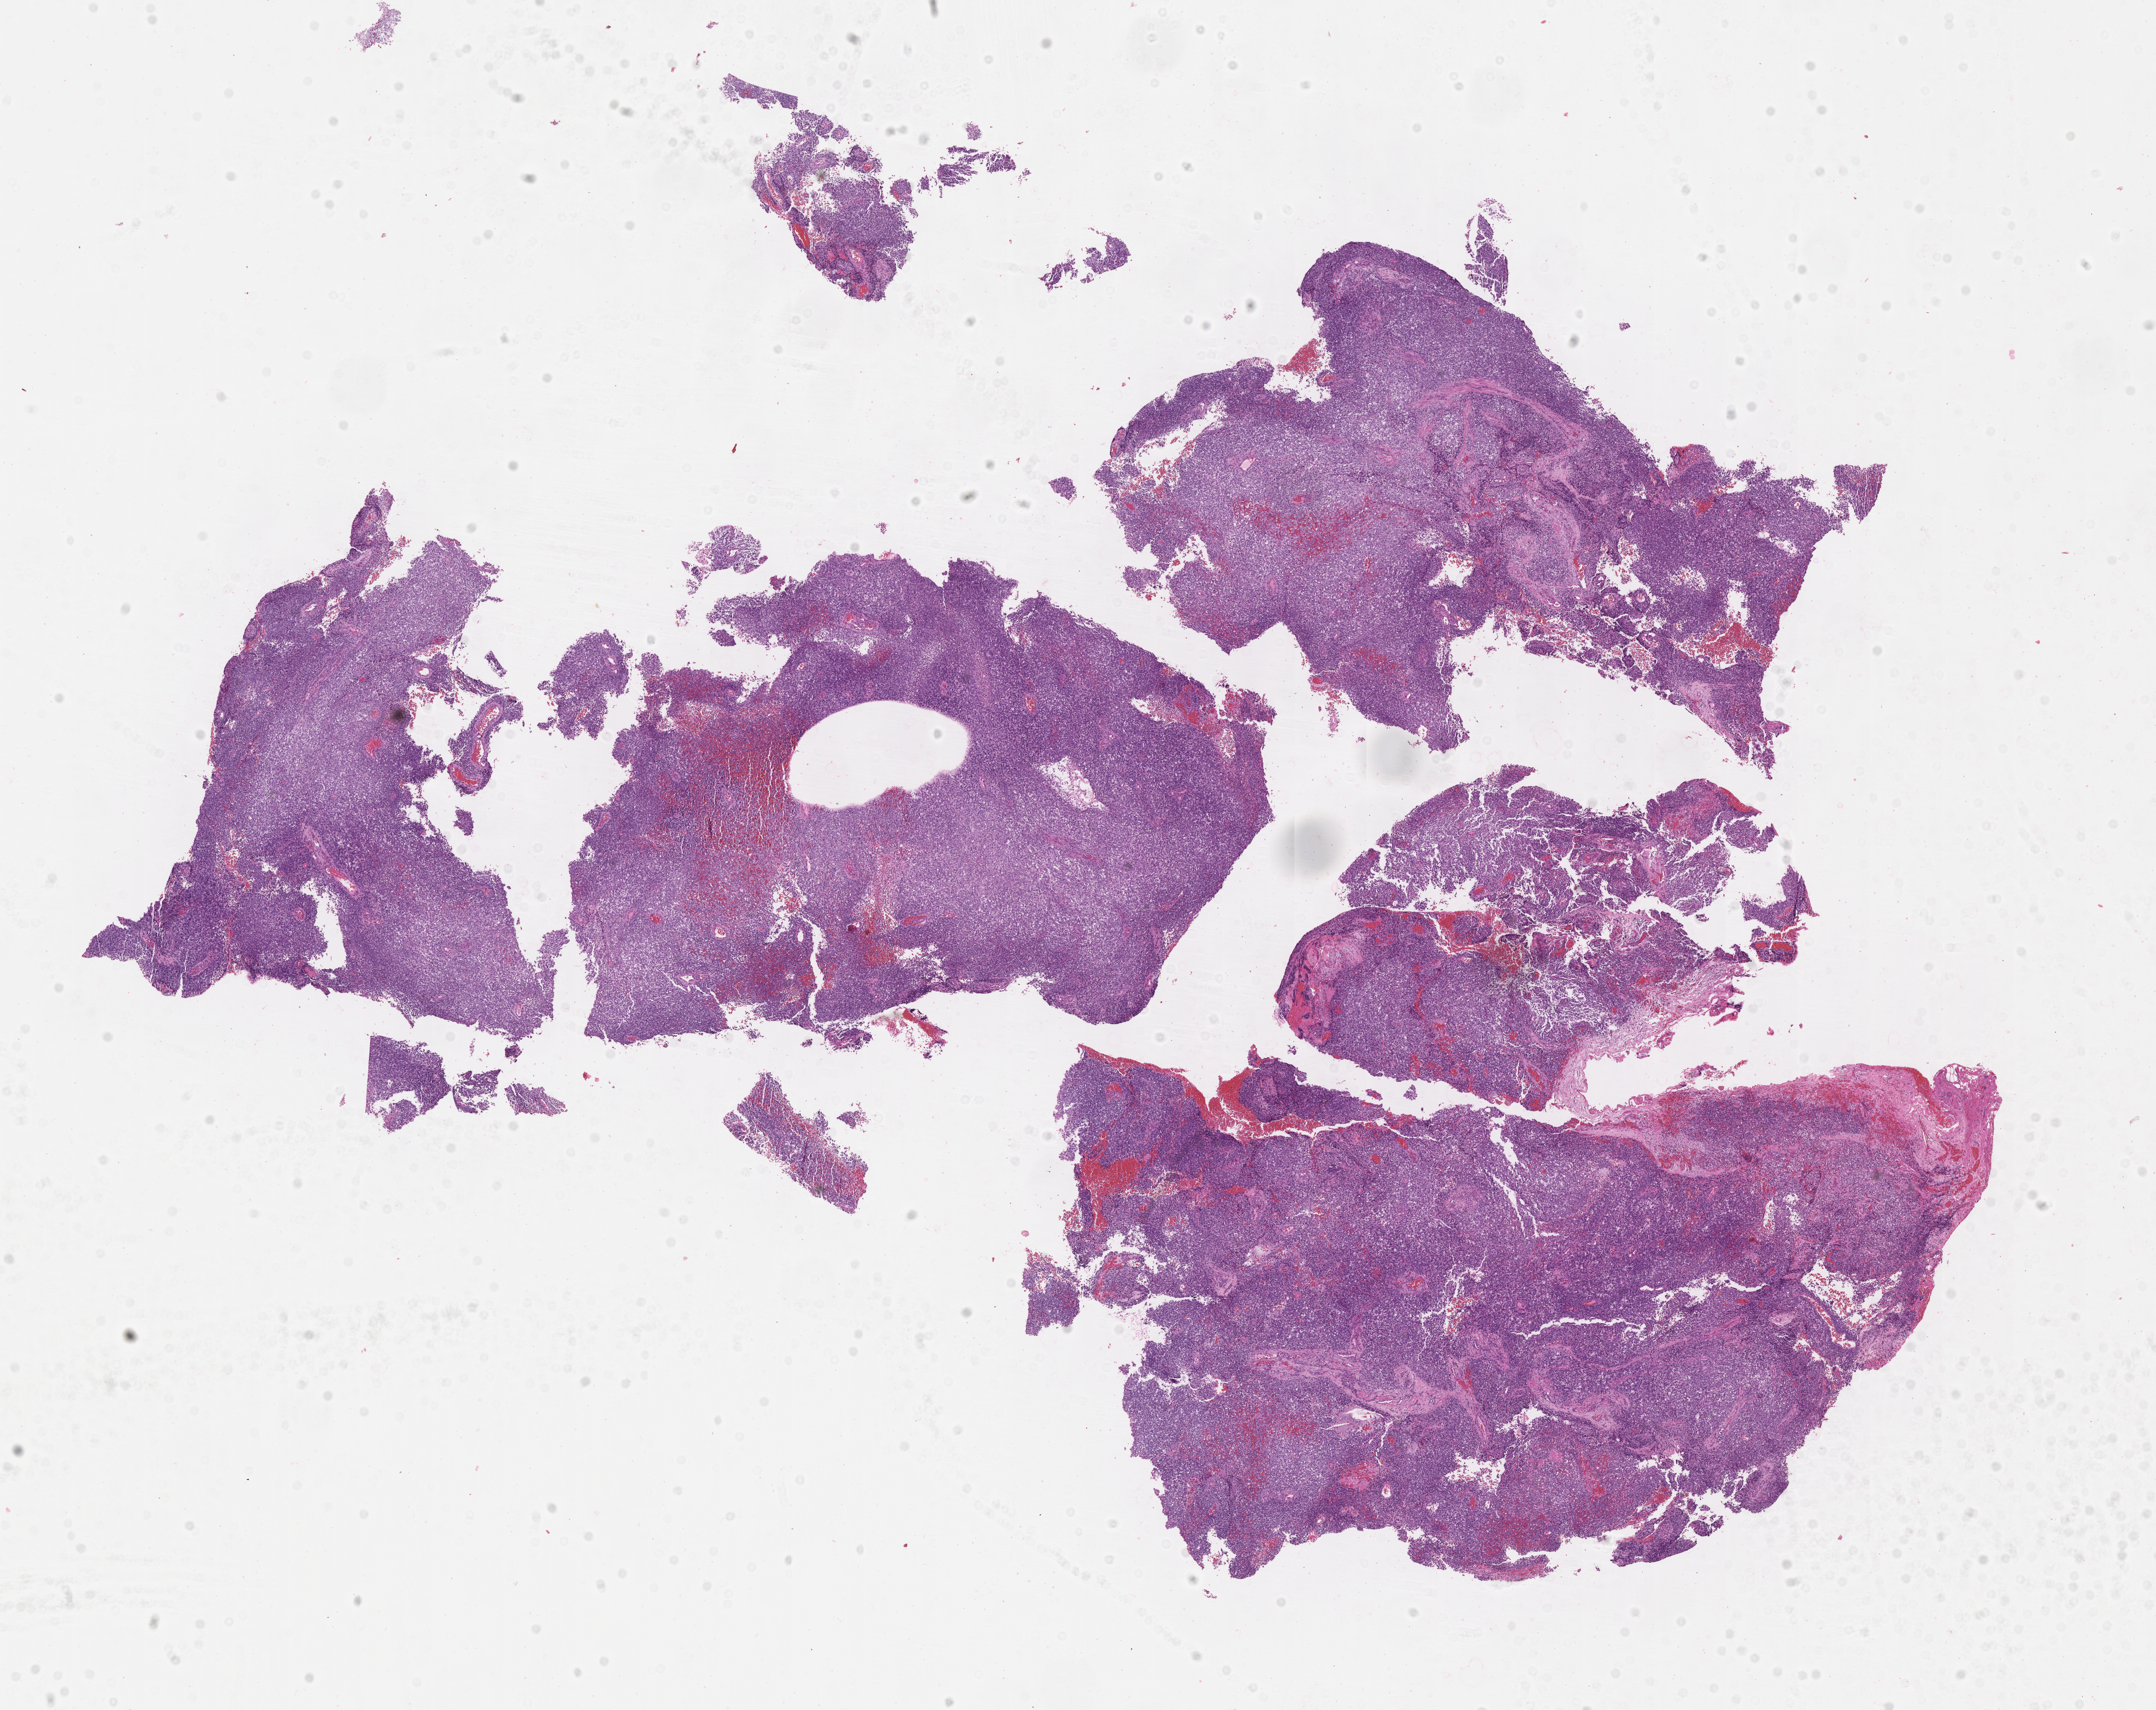
Whole-slide image, haematoxylin and eosin stain of tumor tissue, whole scanned area (about 15.1 x 12.0 mm) shown as a low-resolution overview. Formalin-fixed paraffin-embedded section. Sample anatomic site: eye - orbit, left. Patient: male, age 7.9 years at diagnosis.
* stage (as recorded): 1
* metastatic status at presentation (as recorded): non-metastatic (unconfirmed)
* diagnosis: rhabdomyosarcoma; histological classification: embryonal rhabdomyosarcoma